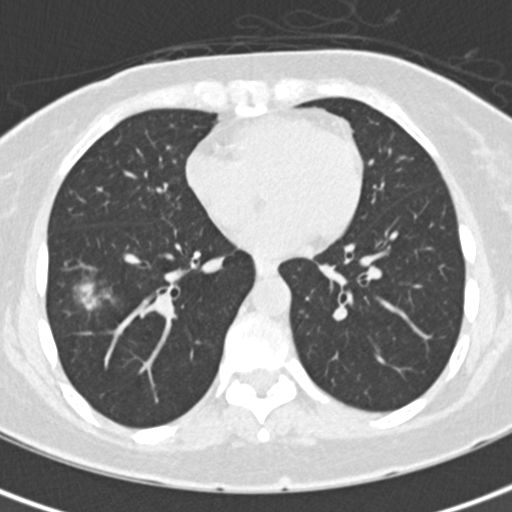
Low-dose screening chest CT, one axial slice. Position 71 of 171 along the scan axis. Reconstruction kernel B30f. Lung window (W 1500 / L -600 HU). 2 mm slice thickness. 512 × 512 image matrix, field of view 284 × 284 mm.
Outlined on this slice (outlined manually by an expert reader):
- lesion 1 (tumor, lower lobe of right lung): bounding box [x1, y1, x2, y2] px = [74, 279, 115, 310]